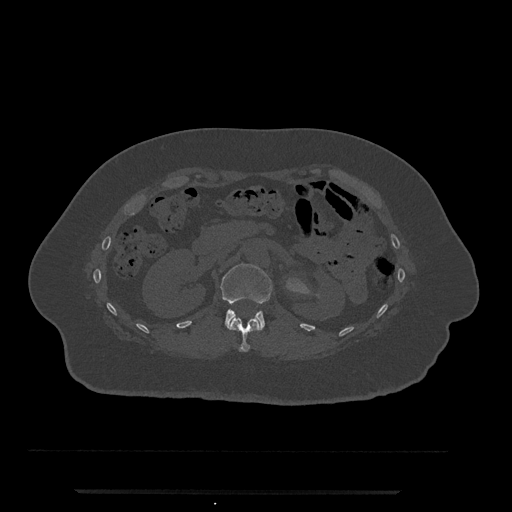
CT including the spine, one axial slice. Slice 131 of 797 in the series (ordered by position). Bone window (W 1800 / L 400 HU). 0.5 mm slice thickness. 512 × 512 image matrix, field of view 440 × 440 mm. Patient: female, 51 years. Case-level facts recorded for this patient, not image findings: primary cancer: neuro; vertebrae with lytic lesions (as recorded): T8.
Annotated regions visible in this slice (semi-automatic segmentation, software-assisted and operator-edited):
- L1 vertebra: box from (x=220, y=264) to (x=273, y=330) px
- T12 vertebra: (x=228, y=318)–(x=261, y=352)